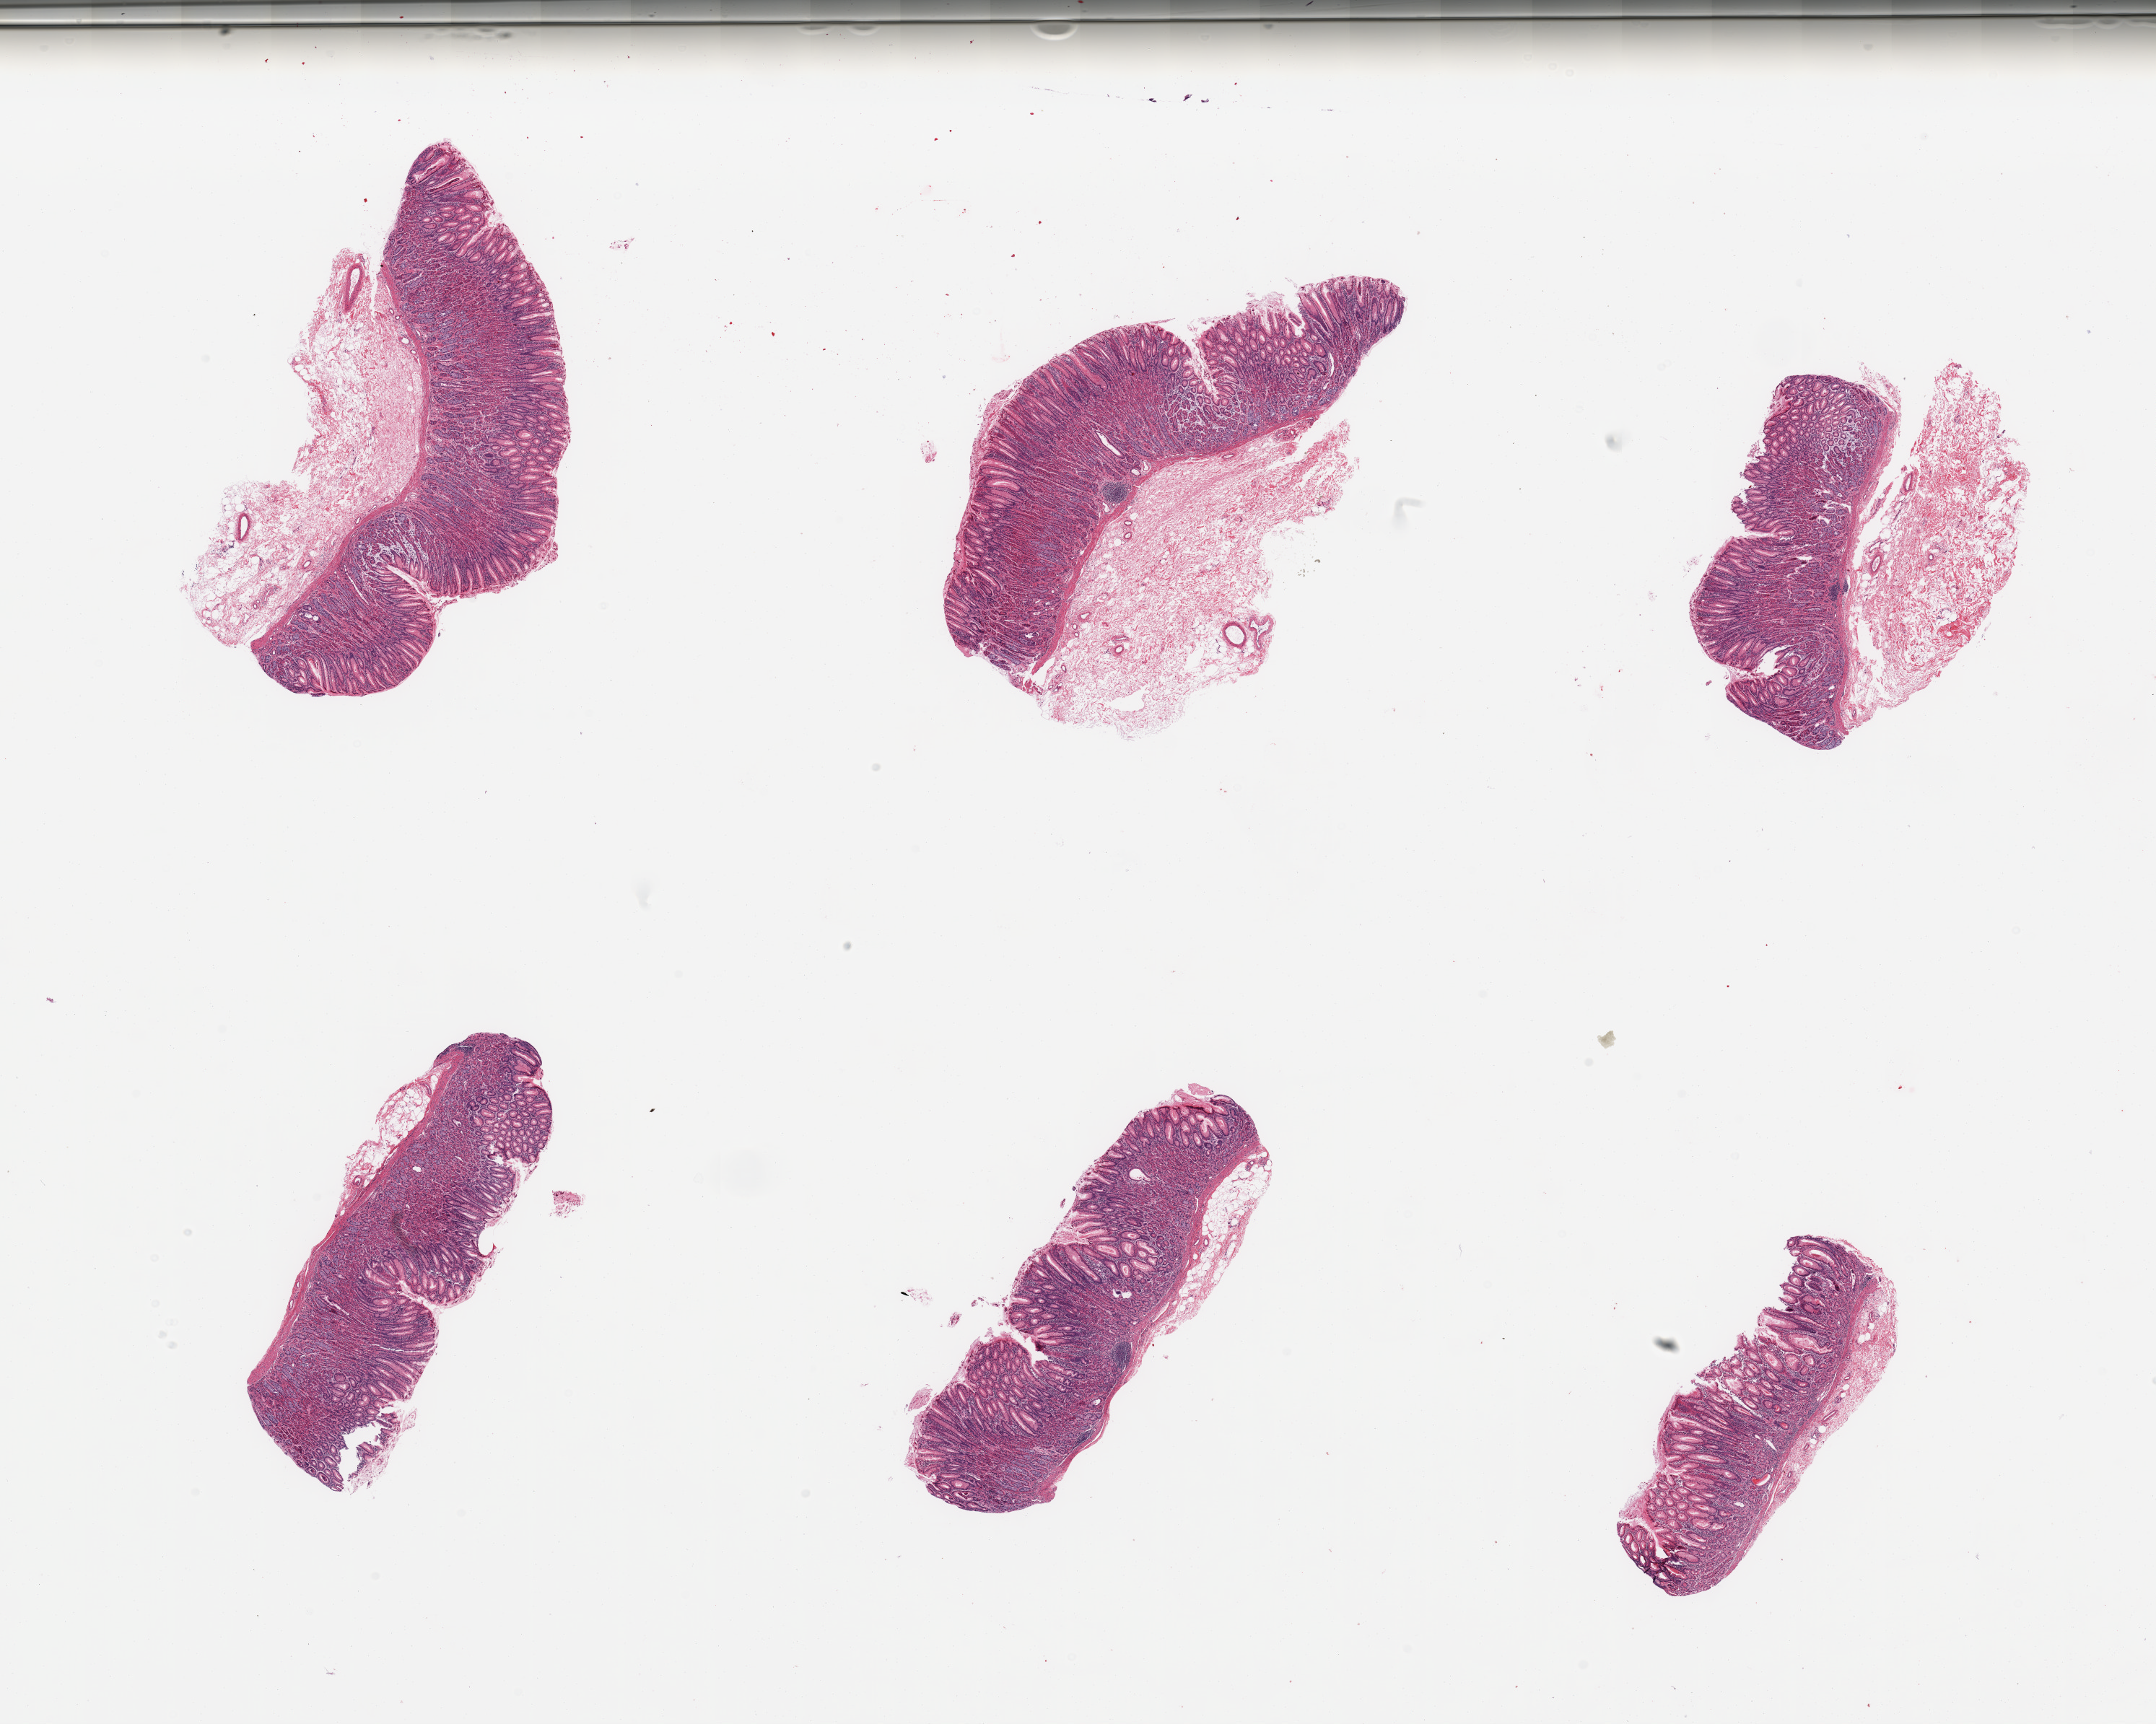
Digitized hematoxylin and eosin (H&E)-stained section, whole scanned area (about 23.6 x 18.9 mm) shown as a low-resolution overview. PAXgene-fixed paraffin-embedded (PFPE) section. Sampled site (target tissue): stomach. Tissue donor sample.
• pathologist's review note for this sample: 6 pieces; mucosa and submucosa